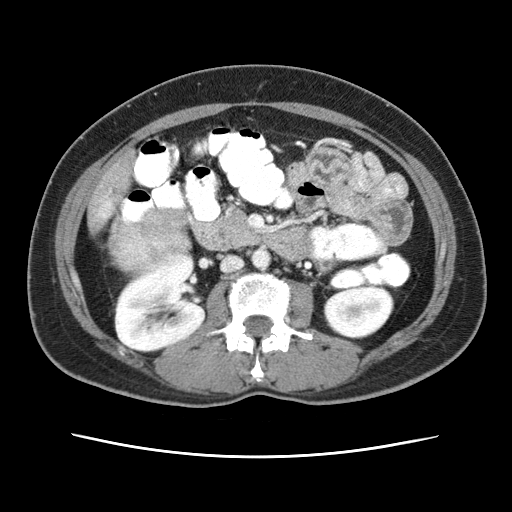
Contrast-enhanced abdominal CT (liver protocol), one axial slice. Reconstruction kernel STANDARD. Soft-tissue window (W 400 / L 40 HU). 2.5 mm slice thickness. 512 × 512 image matrix. From the clinical record (not read from this slice): diagnosis: hepatocellular carcinoma (patient treated with transarterial chemoembolisation; whether this scan precedes or follows treatment is not stated here); TNM stage (as recorded): Stage-I; Child-Pugh class: A; tumour nodularity: uninodular.
Outlined on this slice (semi-automatic segmentation, software-assisted and operator-edited):
- abdominal aorta: box from (x=252, y=250) to (x=270, y=270) px
- liver parenchyma outside the tumour (the mass and vessels are separate outlines, so this box may not span the whole liver): (x=92, y=153)–(x=132, y=223)
- mass: (x=116, y=212)–(x=184, y=268)